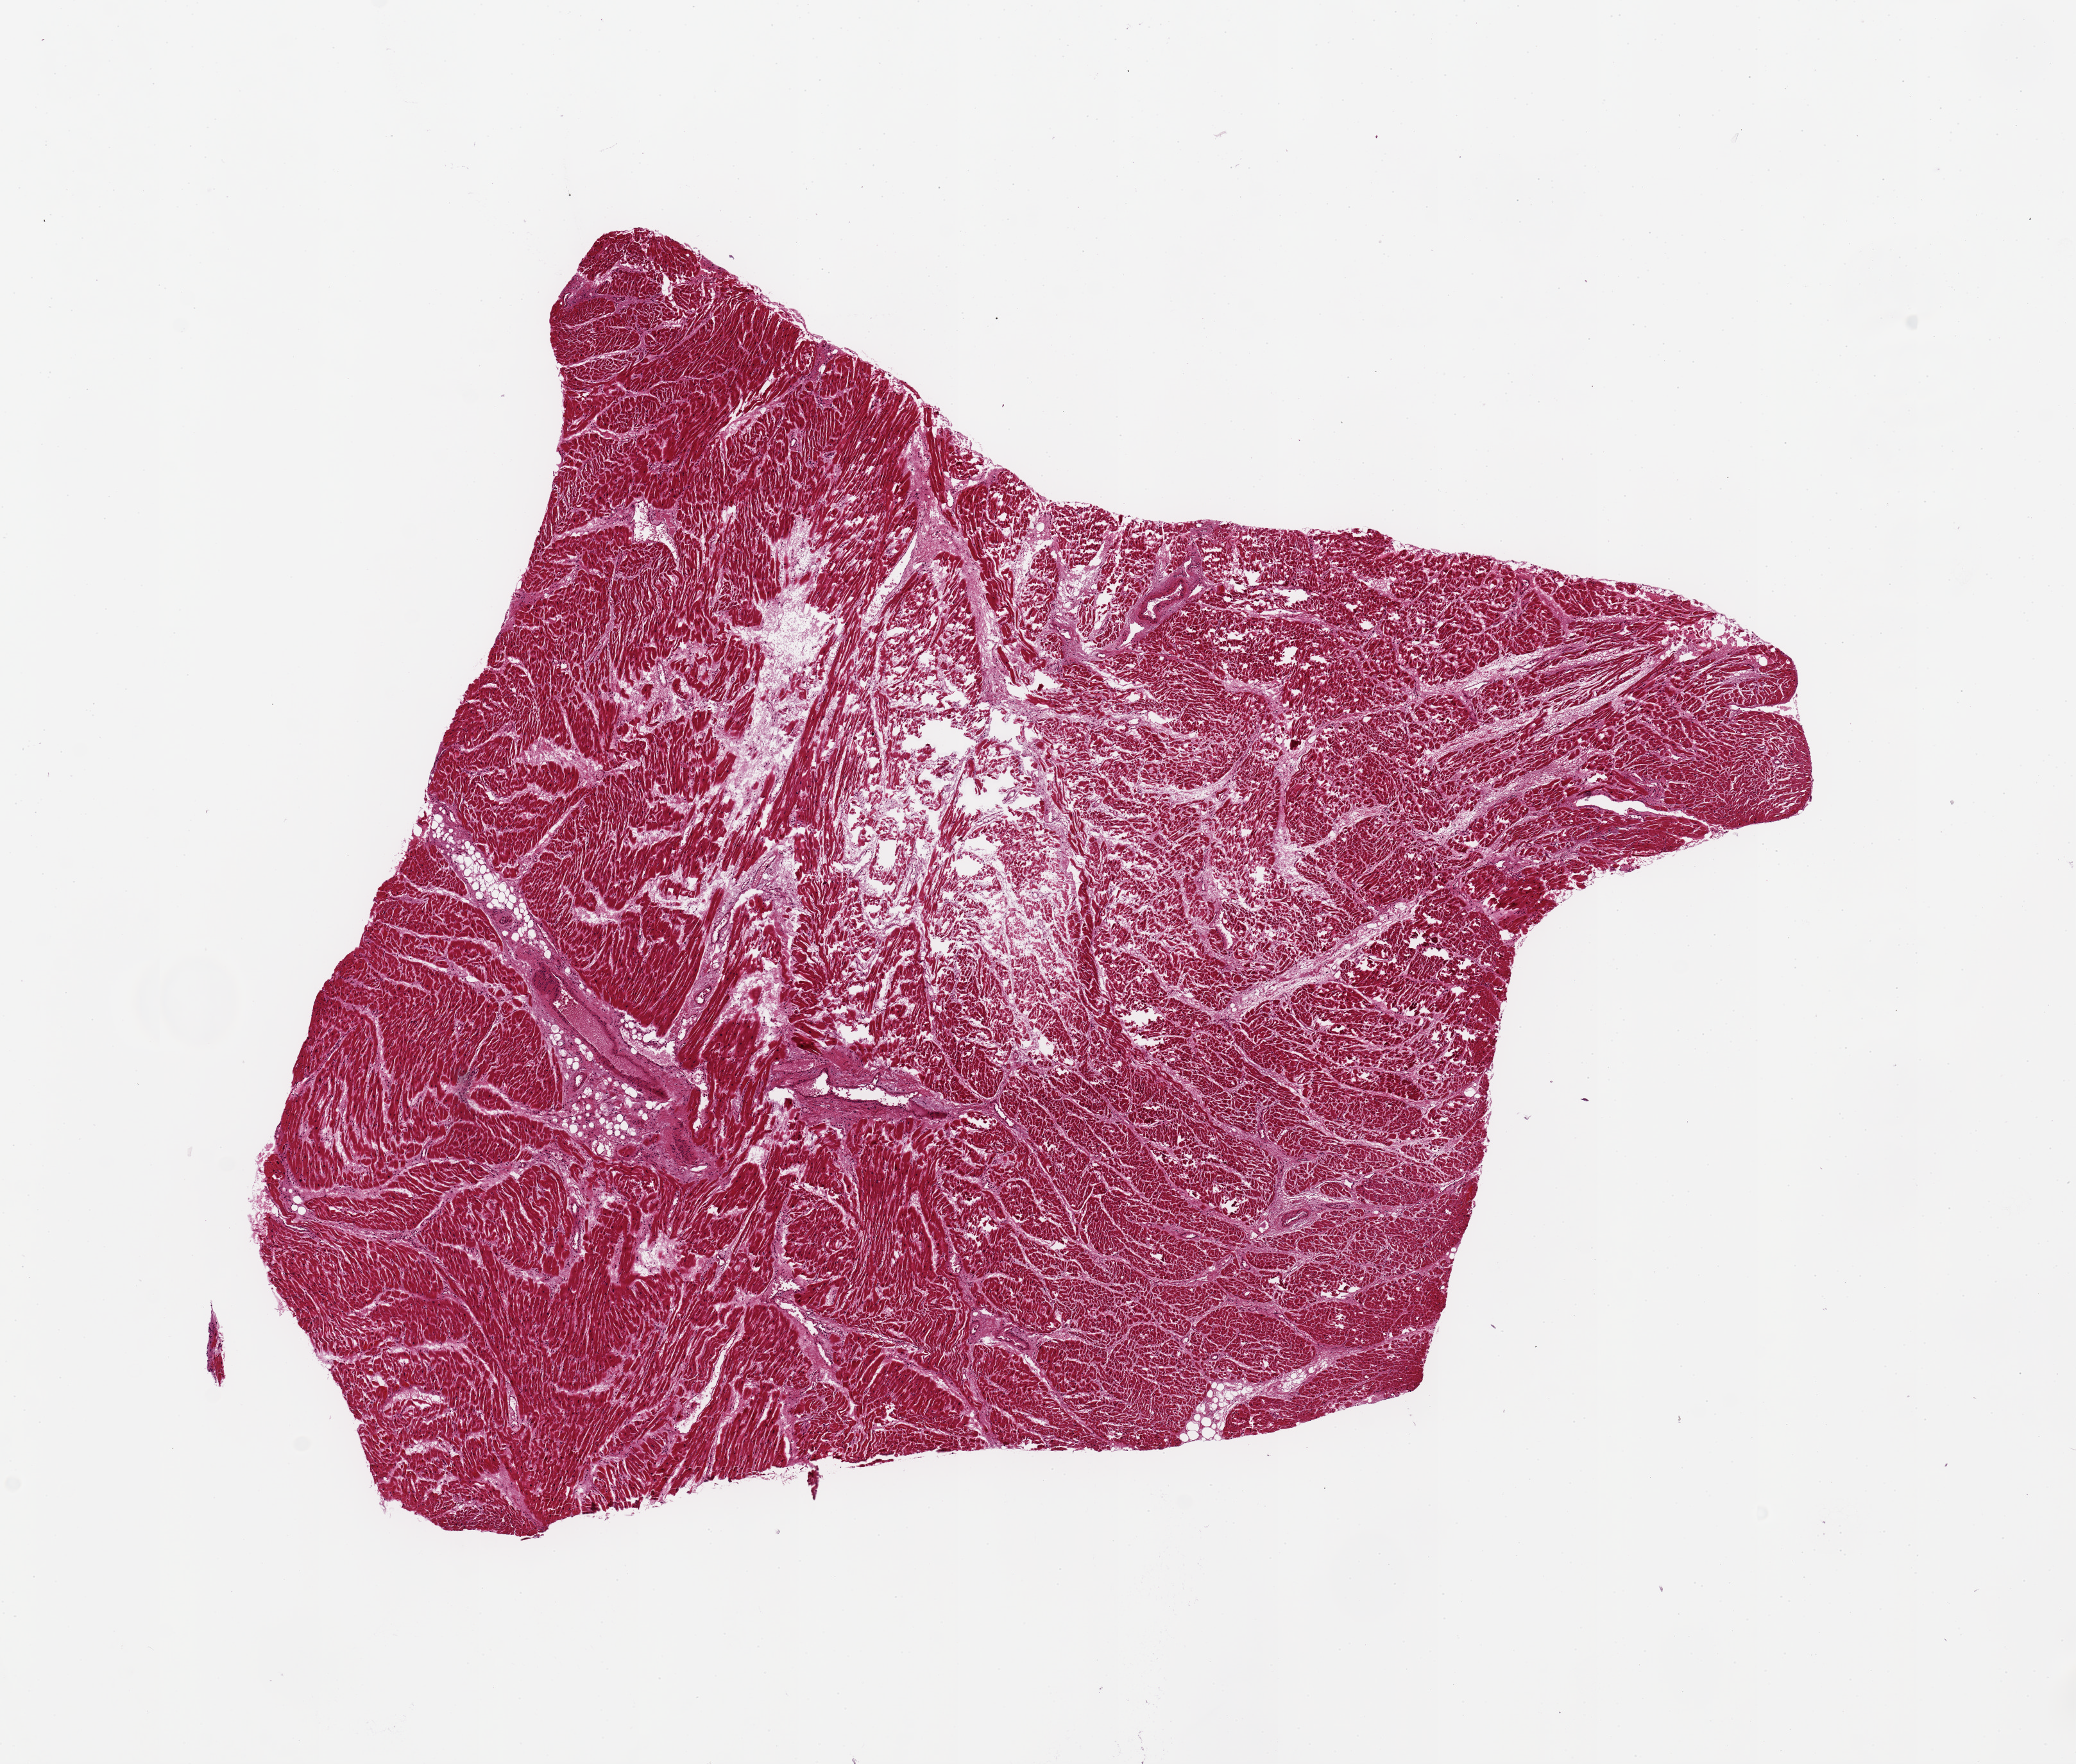
Whole-slide image, H&E stain, brightfield — a low-resolution overview of the entire scanned area, about 12.8 x 10.9 mm (from a 20x scan). PAXgene-fixed paraffin-embedded (PFPE) section. Target tissue: heart. Tissue donor sample. Donor sex: male.
Reviewer comment on this tissue sample: 9.3x8.2. Centrally poorly fixed/ autolytic: doubt infarct as no inflammation noted, pending glass review.